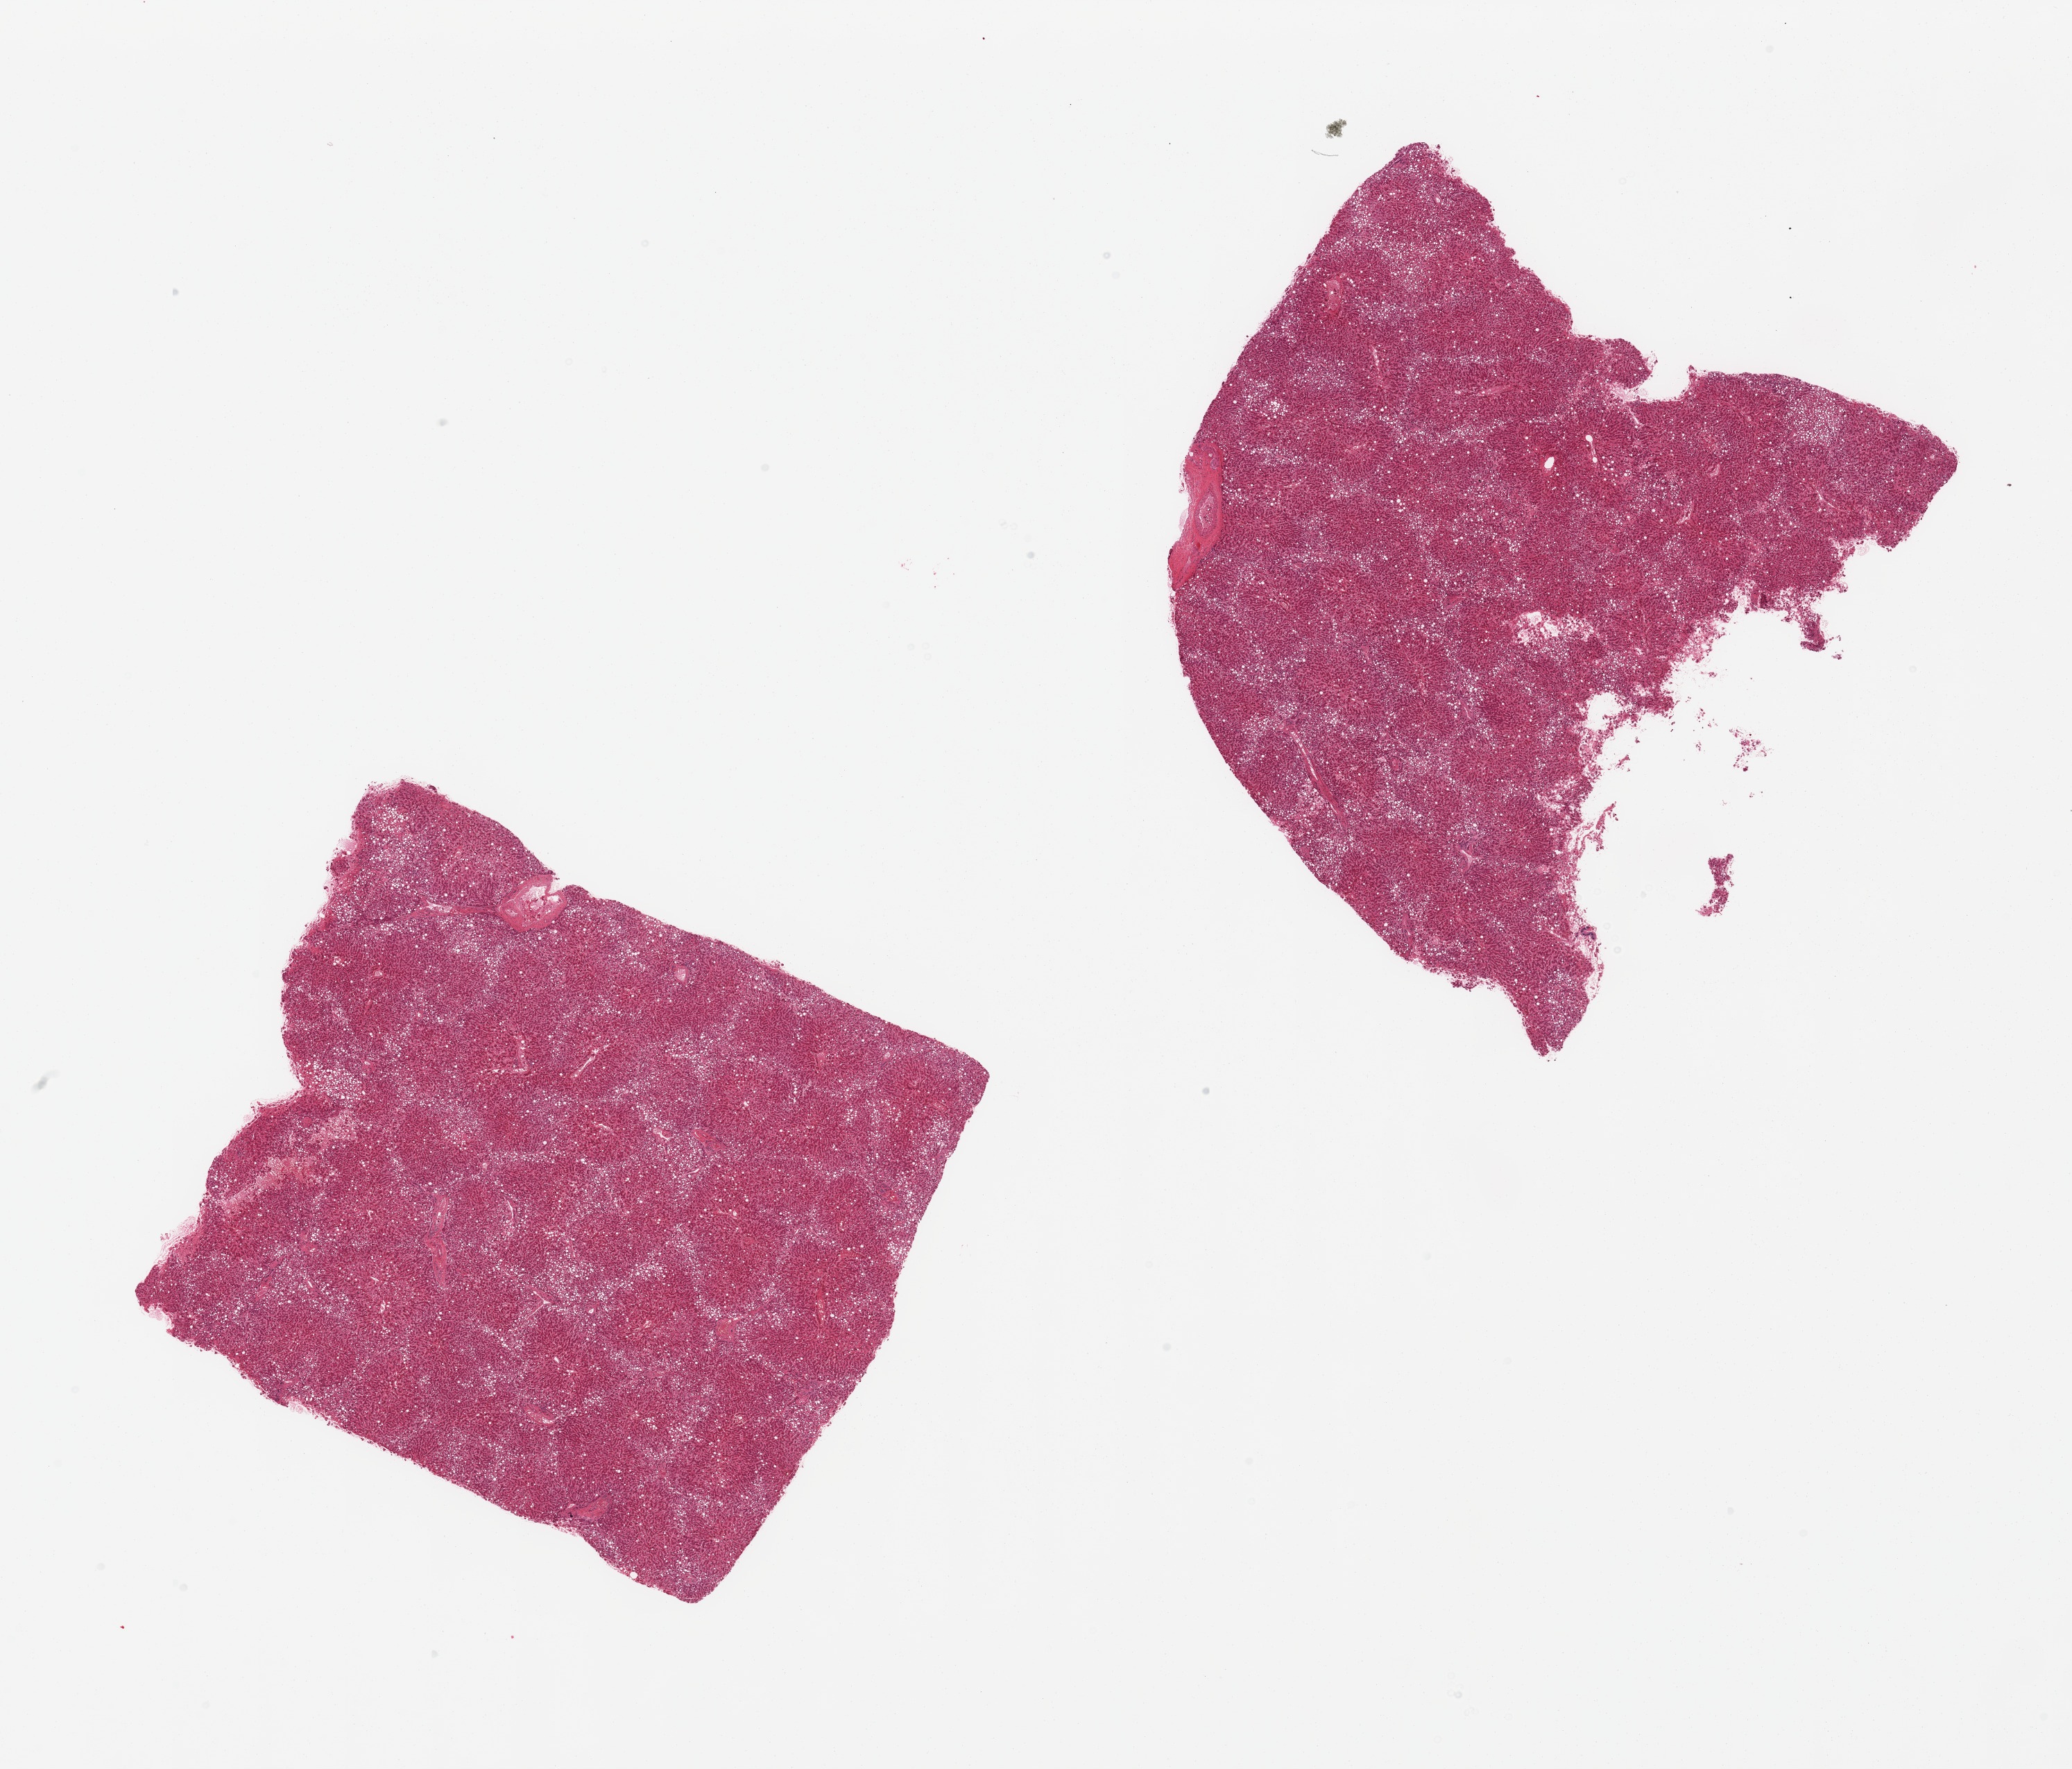
H&E whole-slide image, a low-resolution overview of the entire scanned area, about 23.6 x 20.2 mm. PAXgene-fixed, paraffin-embedded tissue. Section of liver (target tissue). Tissue donor sample. Donor sex: female.
Pathologist's review note for this sample: 2 pieces, moderate-marked diffuse macrovesicular steatosis.